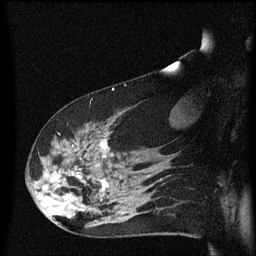
Breast MRI (dynamic contrast-enhanced), one sagittal slice; slice 38 of 60 in the series (ordered by position); dynamic contrast-enhanced series, image 2 of 3 at this slice position (ordered by acquisition); 1.5 T; TE 4.2 ms, TR 8.4 ms; 2 mm slice thickness; 256 × 256 image matrix, field of view 200 × 200 mm. Patient: female, 48 years.
Annotated regions visible in this slice (semi-automatically segmented with operator editing):
- analysis volume of interest (the breast-tissue region the enhancement analysis was run in; not a lesion): bounding box <31,116,134,225> (left, top, right, bottom; pixels)
- tumour enhancement mask (voxels above the 70 % enhancement threshold inside the analysis volume of interest): <63,140,107,201>